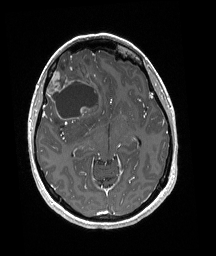
Brain MRI from a brain-tumour surgery series, one axial slice. Slice 110 of 192 in the series (ordered by position). T1-weighted post-contrast. 216 × 256 image matrix, field of view 211 × 250 mm. From the clinical record (not read from this slice): histopathology: Oligodendroglioma; WHO grade: 3; IDH mutation: yes; tumour location: Right Frontal.
Annotated regions visible in this slice (manually delineated by an expert):
- tumour: bounding box <46,51,98,125> (left, top, right, bottom; pixels)